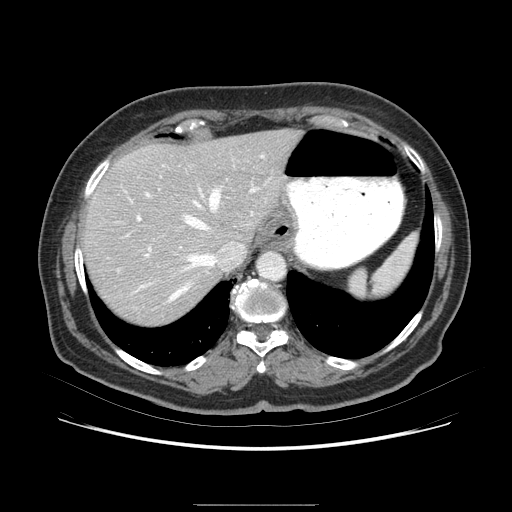
Contrast-enhanced abdominal CT (liver protocol), one axial slice; slice 62 of 79 in the series (ordered by position); 120 kVp; soft-tissue window (W 400 / L 40 HU); 512 × 512 image matrix, field of view 380 × 380 mm. From the clinical record (not read from this slice): diagnosis: hepatocellular carcinoma (patient treated with transarterial chemoembolisation; whether this scan precedes or follows treatment is not stated here); TNM stage (as recorded): Stage-I; Child-Pugh class: A; tumour differentiation: poorly differentiated; tumour nodularity: uninodular.
Outlined on this slice (semi-automatic segmentation, software-assisted and operator-edited):
- liver parenchyma outside the tumour (the mass and vessels are separate outlines, so this box may not span the whole liver): box from (x=86, y=136) to (x=304, y=306) px
- liver vessels: (x=137, y=163)–(x=299, y=264)